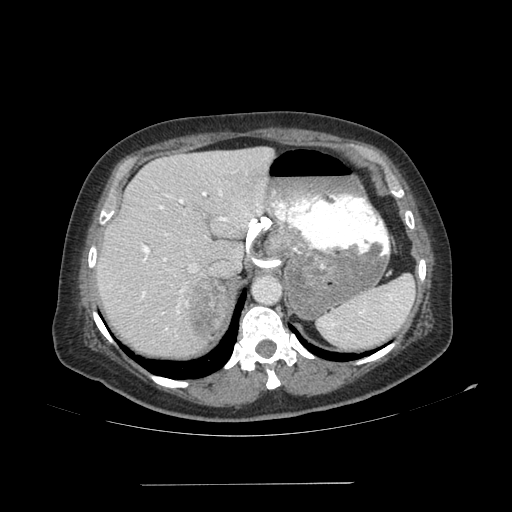
Contrast-enhanced abdominal CT, one axial slice; position 79 of 113 along the scan axis; reconstruction kernel SOFT; soft-tissue window (W 400 / L 40 HU); 2.5 mm slice thickness; 512 × 512 image matrix, field of view 440 × 440 mm. Patient: female, 67 years. From the clinical record (not read from this slice): diagnosis: adrenocortical carcinoma; tumour side: right adrenal; tumour size at pathology: 9.8 cm; Ki-67 index: 59 %; stage (as recorded): 4.
Annotated regions visible in this slice (semi-automatic segmentation, software-assisted and operator-edited):
- mass: bounding box <187,278,228,335> (left, top, right, bottom; pixels)